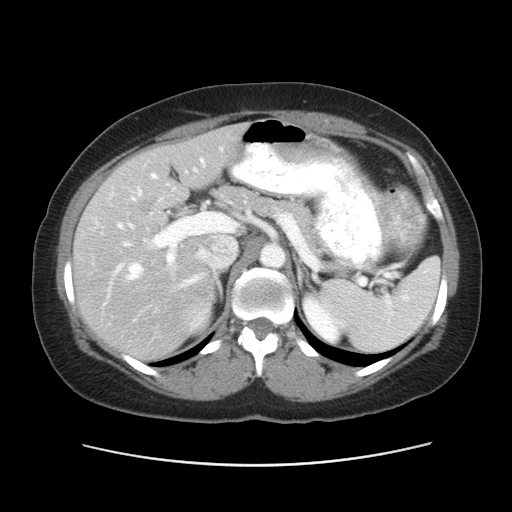
Contrast-enhanced abdominal CT, one axial slice. Slice 33 of 52 in the series (ordered by position). Reconstruction kernel STANDARD. Soft-tissue window (W 400 / L 40 HU). 5 mm slice thickness. 512 × 512 image matrix, field of view 362 × 362 mm. Female patient, age 48 years. From the clinical record (not read from this slice): diagnosis: colorectal cancer liver metastases, imaged before liver resection; multiple liver metastases: yes.
Outlined on this slice (outlined manually by an expert reader):
- hepatic veins: bounding box [x1, y1, x2, y2] px = [128, 148, 223, 288]
- liver: [74, 126, 242, 356]
- planned liver remnant (the part of the liver to remain after resection): [158, 126, 243, 196]
- portal vein (with intrahepatic branches): [107, 159, 211, 296]
- liver metastasis: [137, 197, 156, 218]